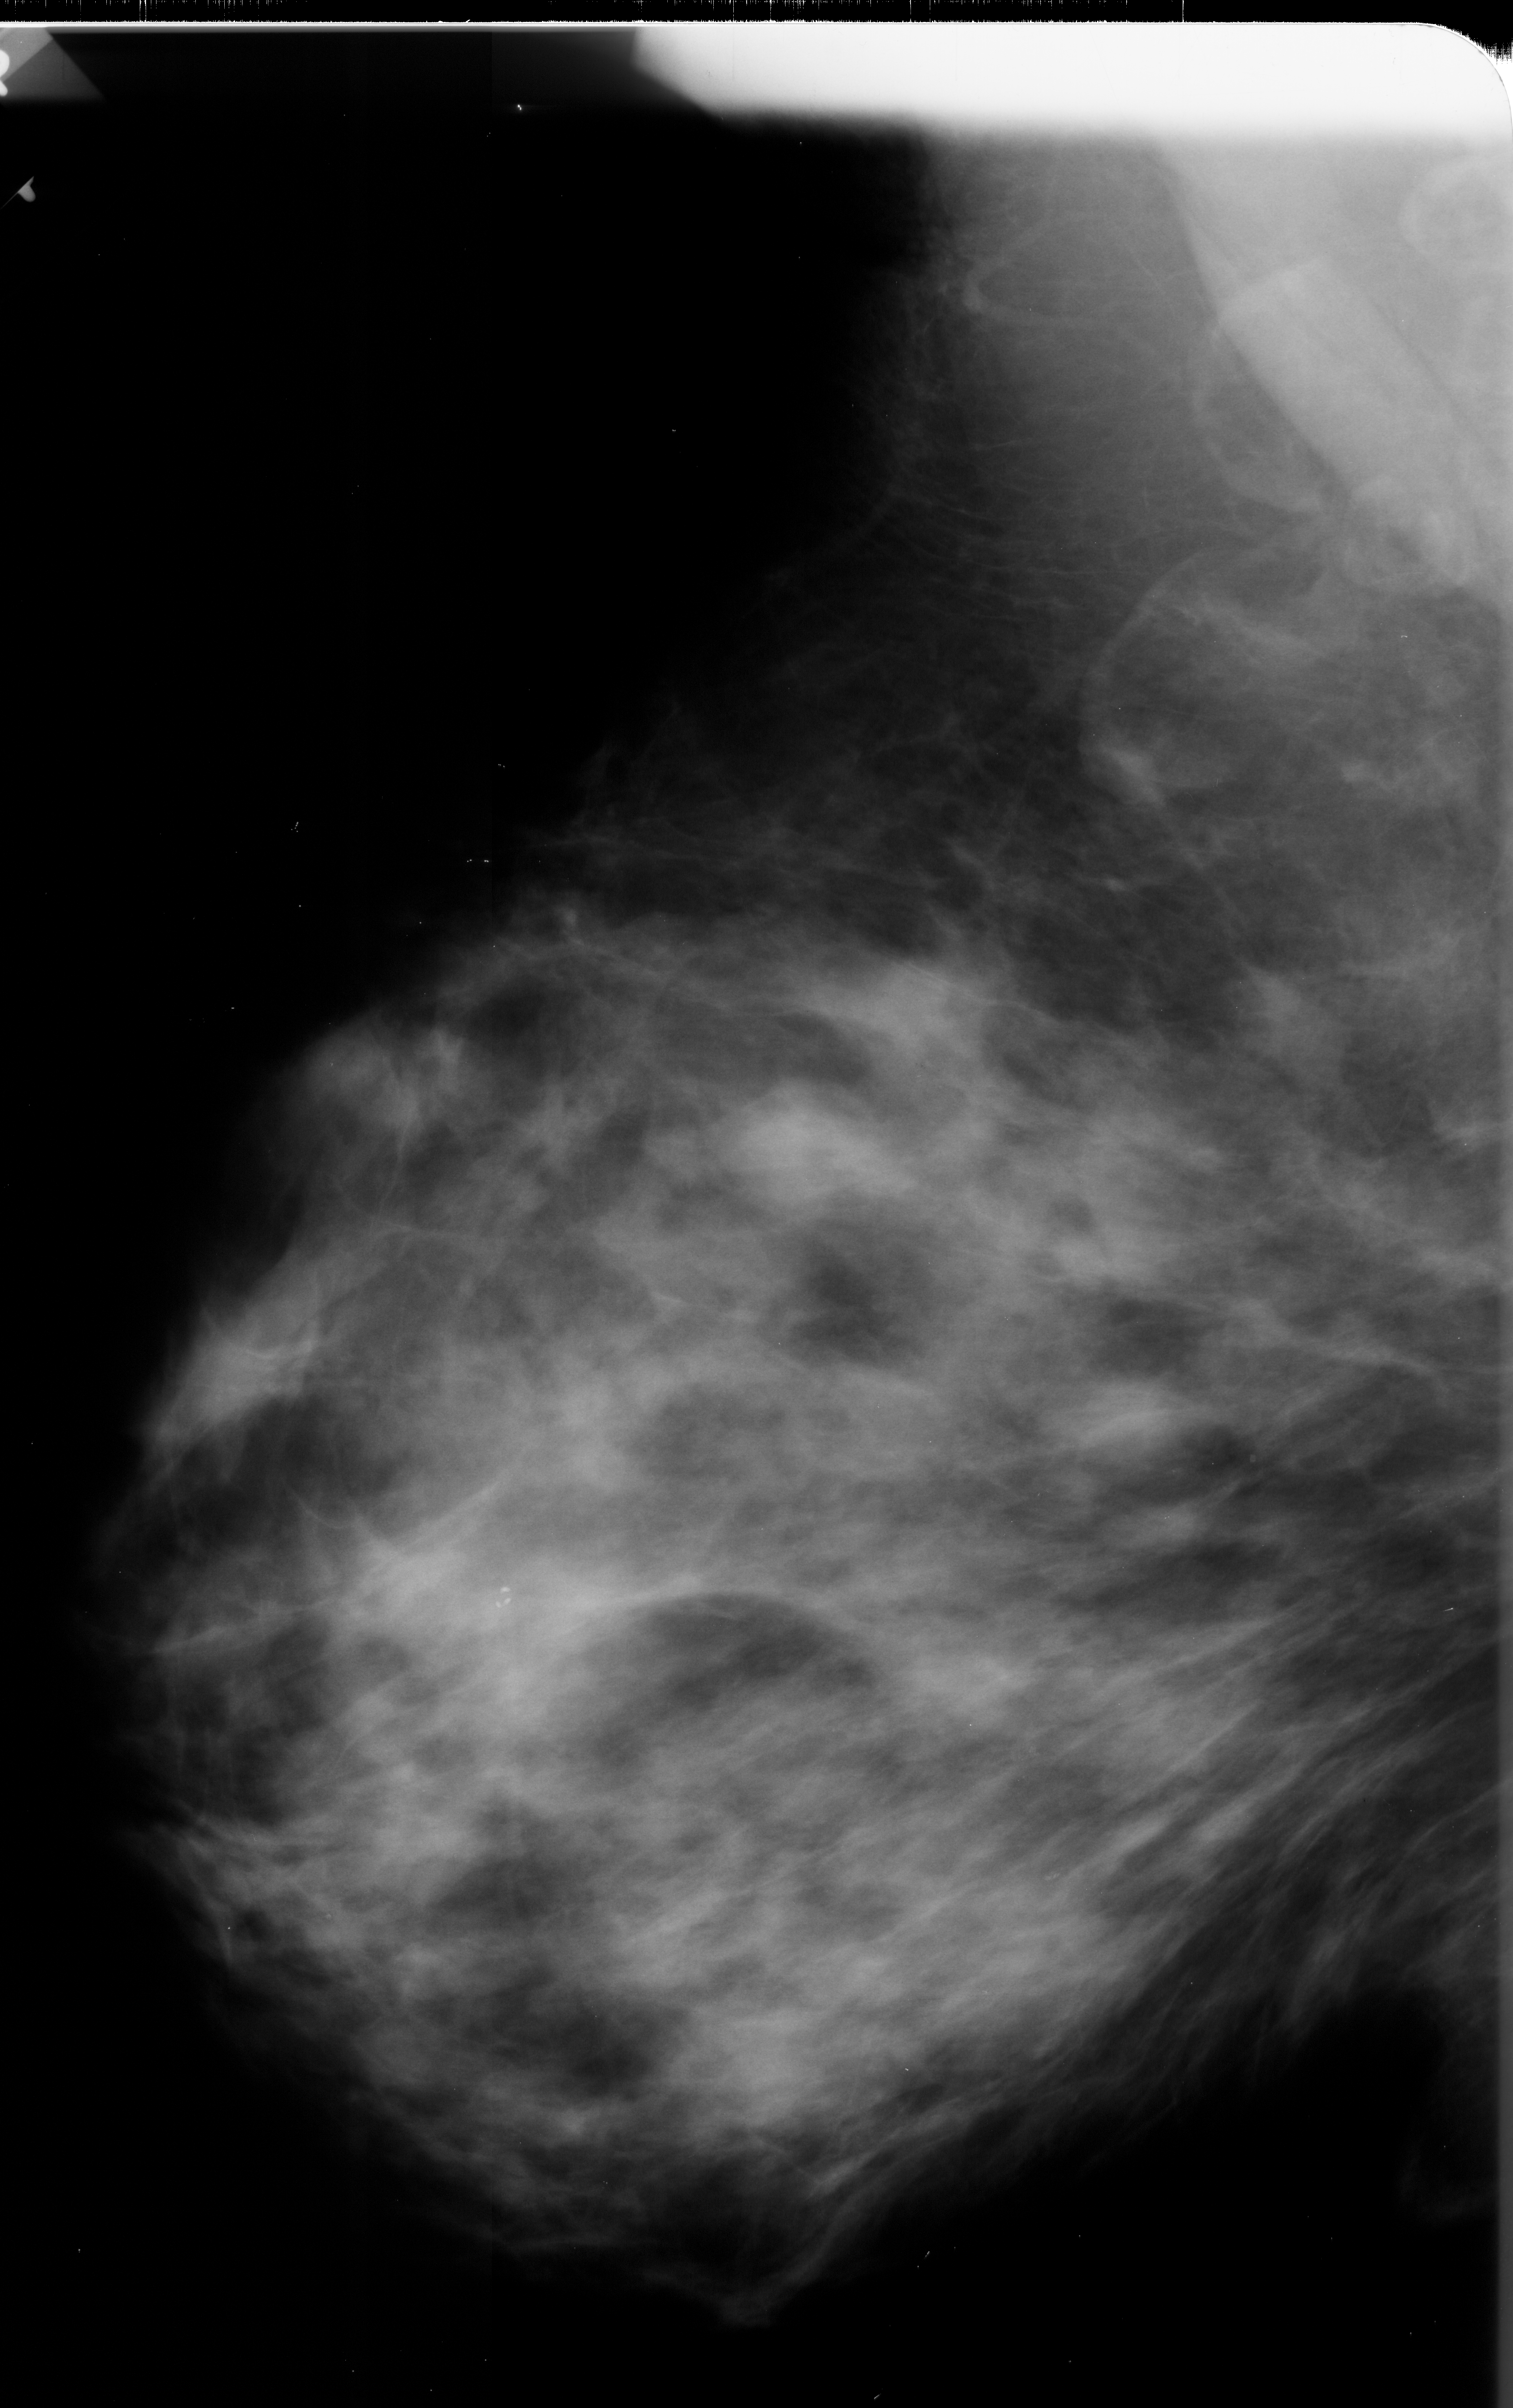
Mammogram (digitized film), left breast, mediolateral oblique (MLO) view, BI-RADS breast density category 4 (scale 1–4).
Calcifications, morphology pleomorphic, distribution linear; BI-RADS assessment category 4; pathology (as recorded): malignant.